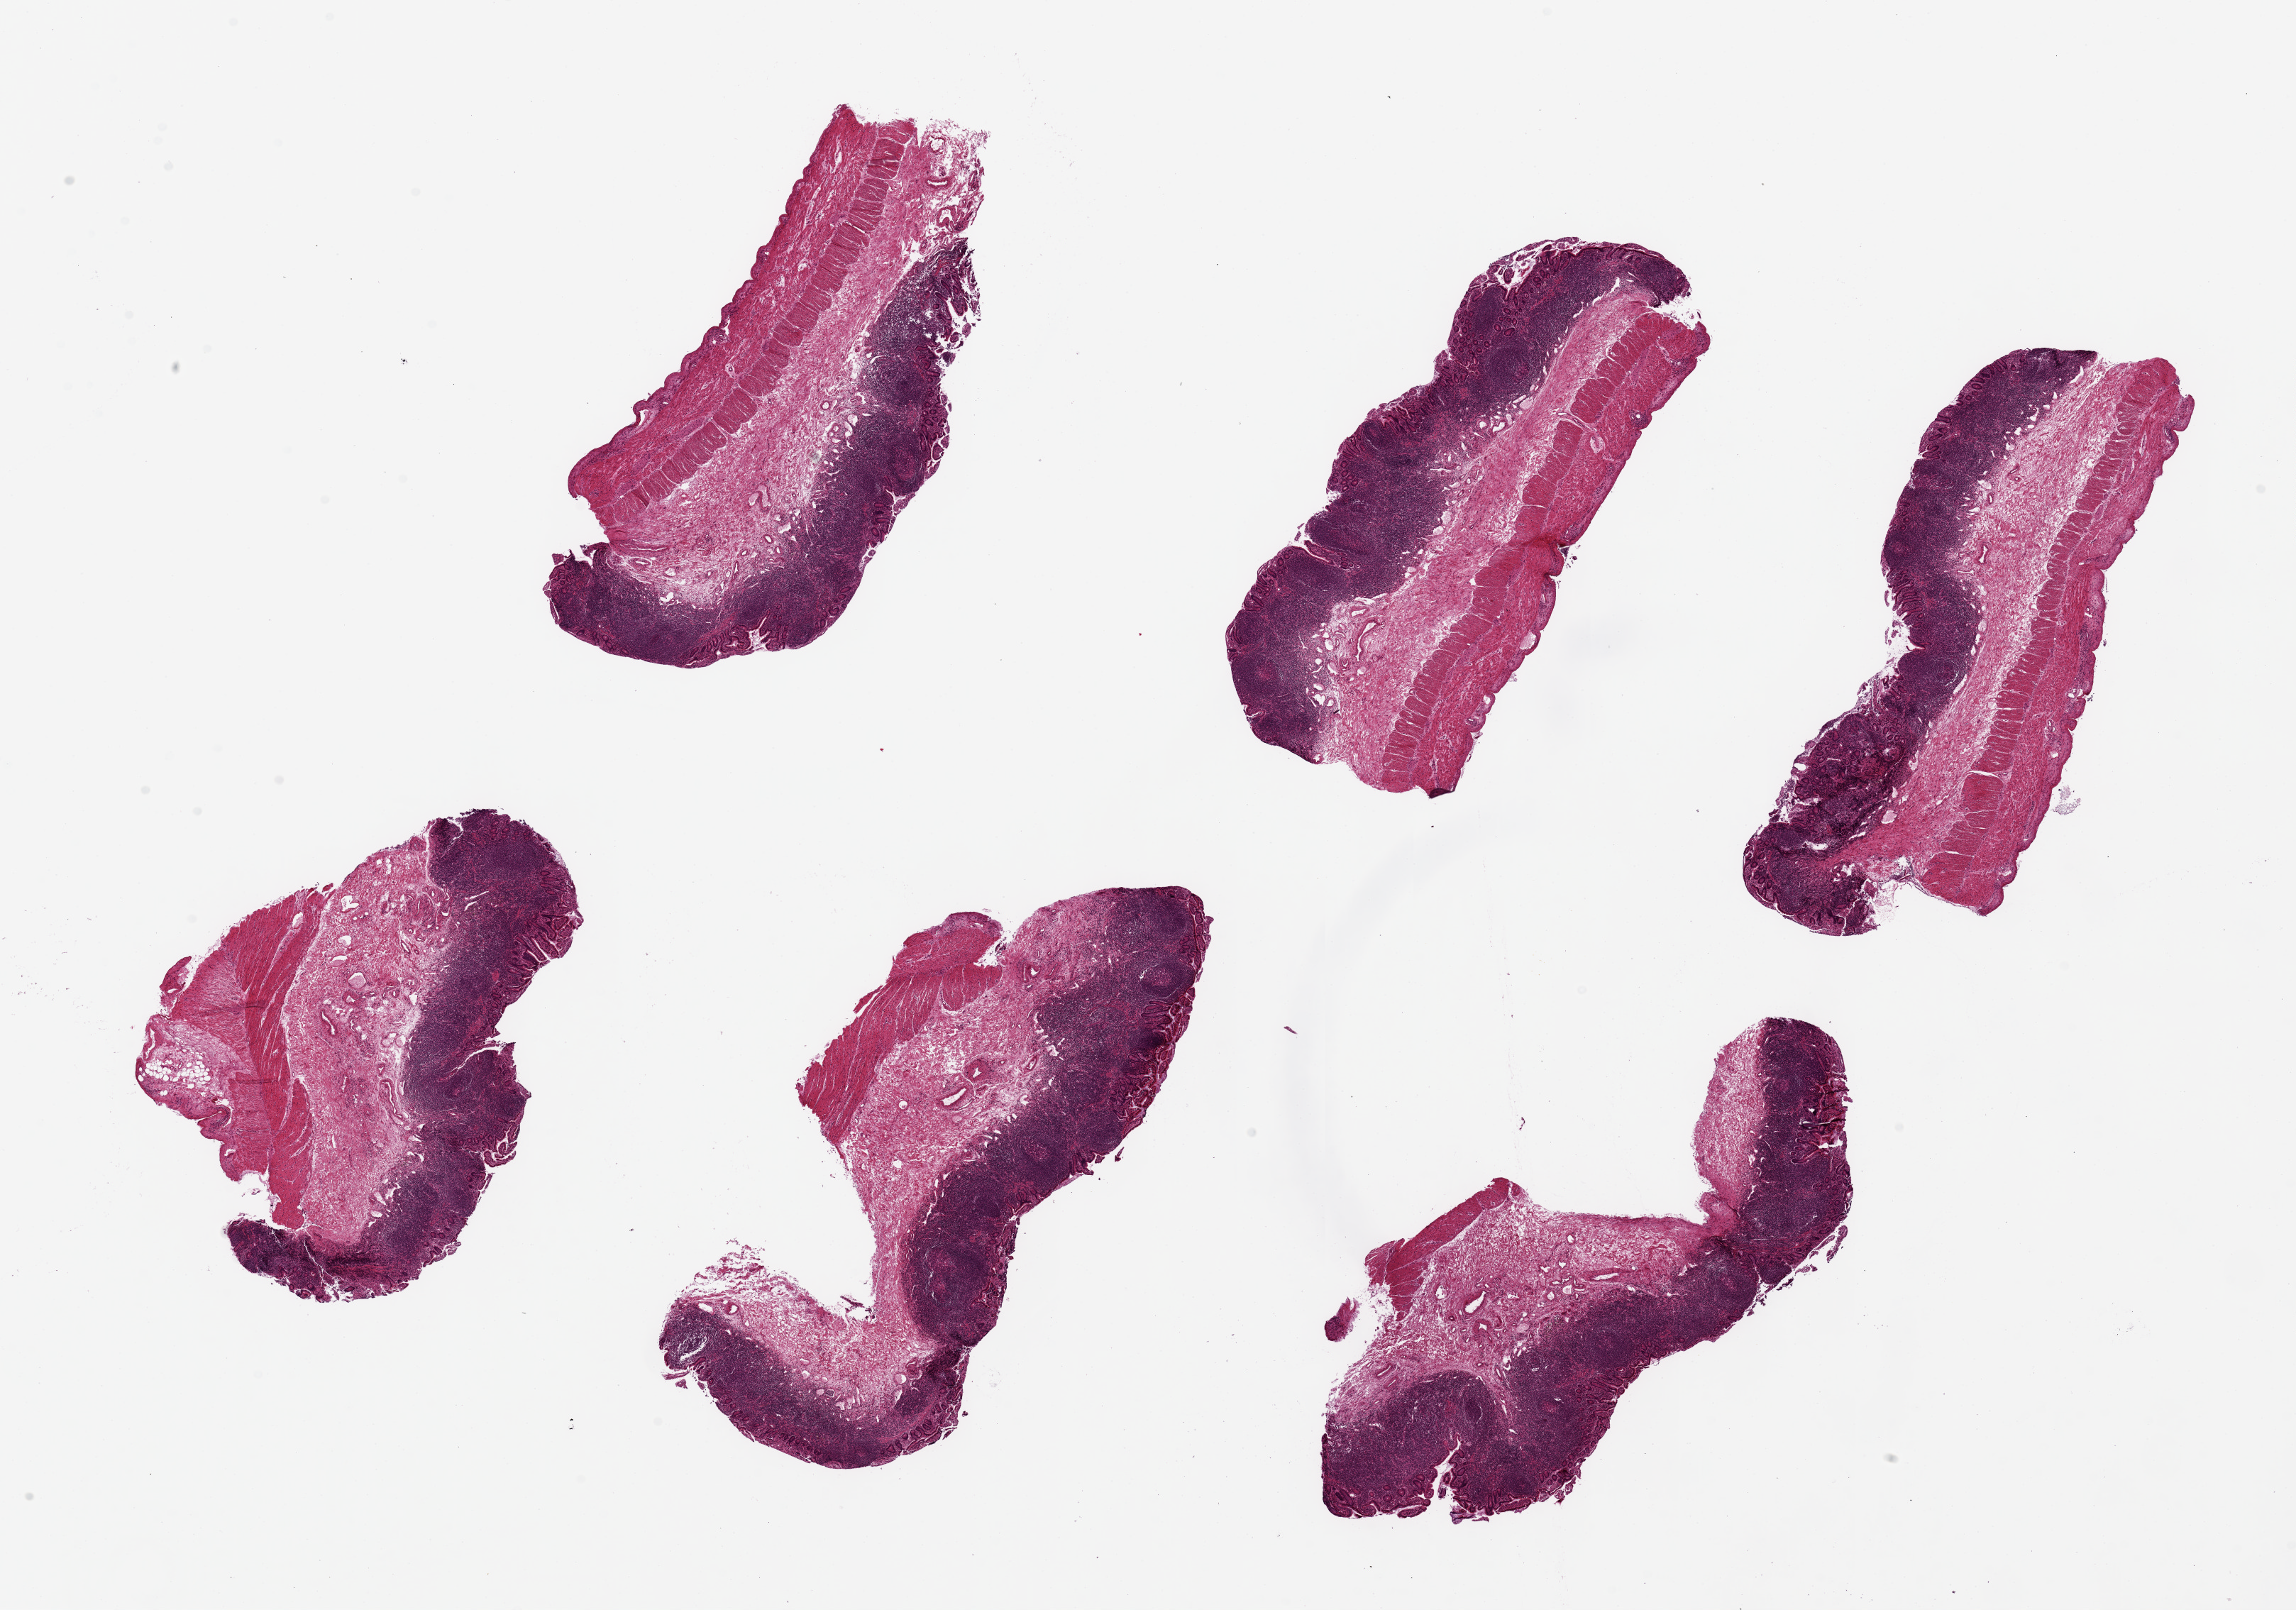
H&E whole-slide image — shown as a low-resolution overview of the whole scanned area (about 25.6 x 17.9 mm, slide scanned at 20x); PAXgene-fixed paraffin-embedded (PFPE) section; sampled site (target tissue): ileum; donor tissue sample. Donor sex: female.
Review note (as recorded): 6 pieces, up to 8x3.5mm; all have abundant lymphoid tissue, BUT all have muscularis propria.